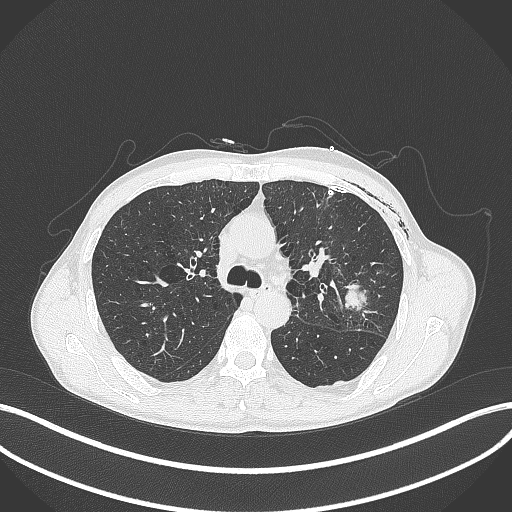
Chest CT, one axial slice; 120 kVp; lung window (W 1500 / L -600 HU); 1 mm slice thickness; 512 × 512 image matrix, field of view 400 × 400 mm. Patient: male, 58 years. Case-level facts recorded for this patient, not image findings: clinical TNM (as recorded): T3 N0 M0.
Annotated regions visible in this slice (bounding box drawn by a radiologist):
- lung tumour (recorded histology: adenocarcinoma): bounding box [x1, y1, x2, y2] px = [338, 275, 370, 318]